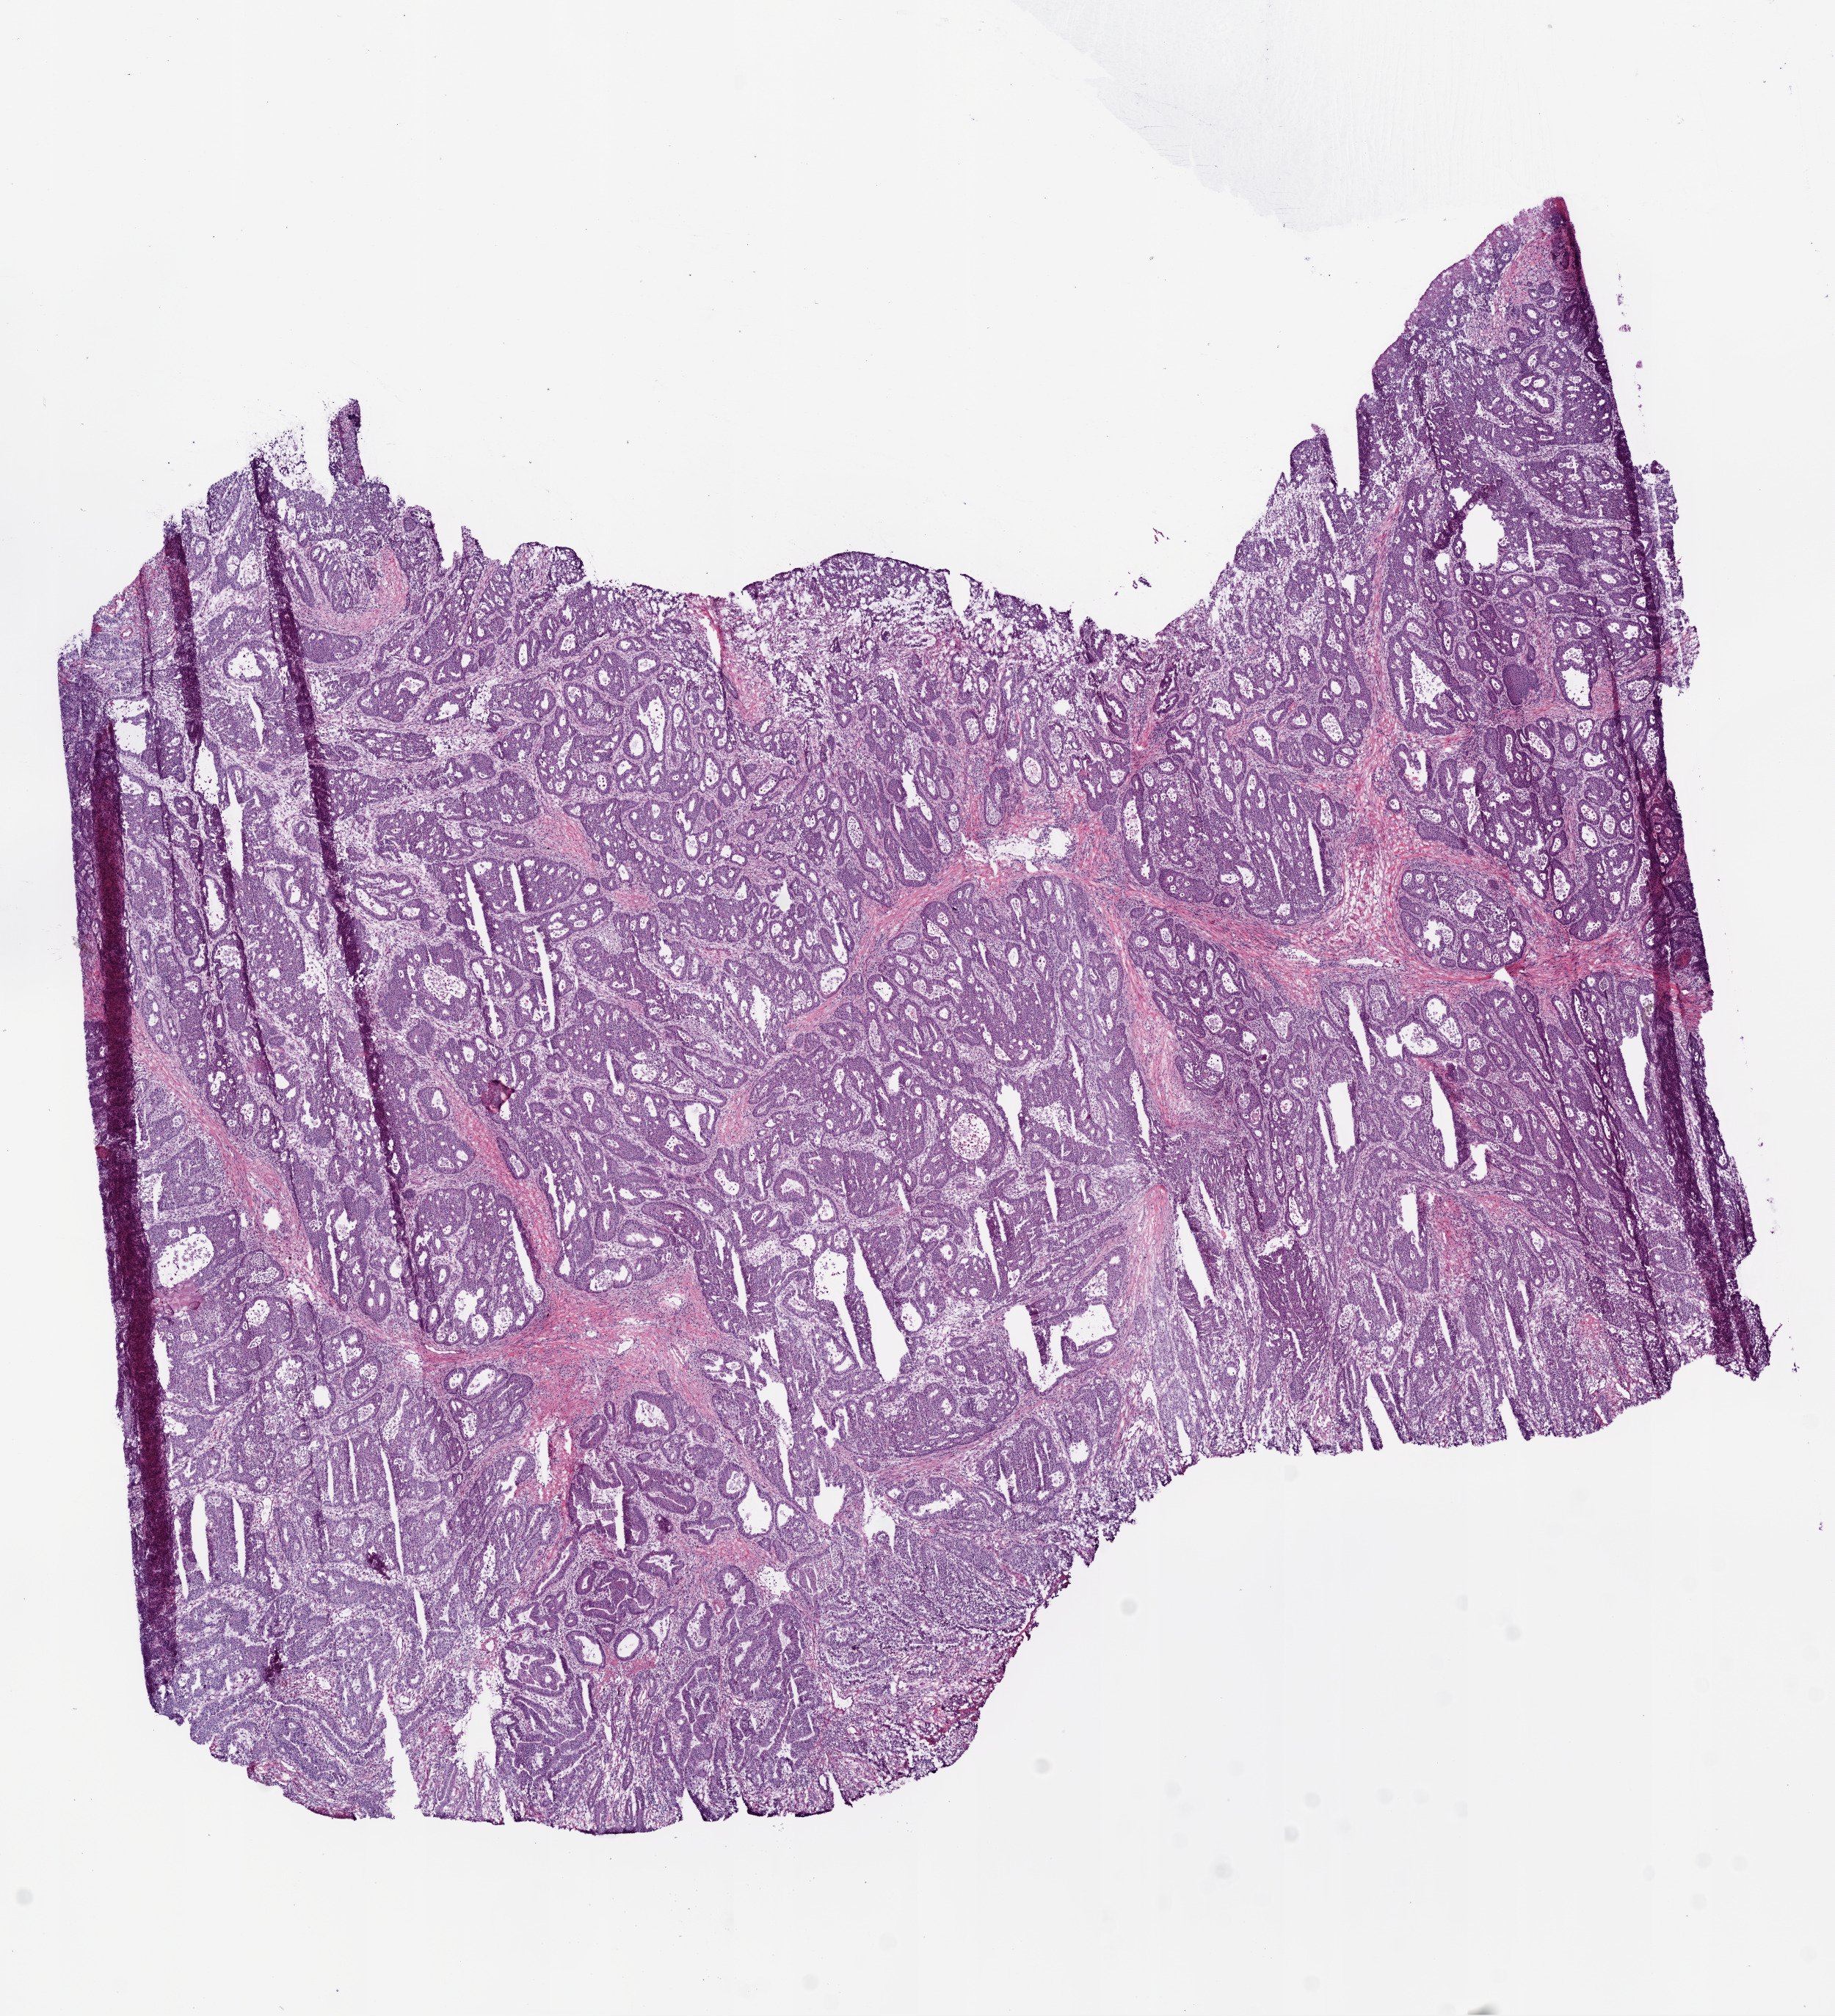
Digitized H&E tissue section (whole slide), a low-resolution overview of the entire scanned area, about 10.0 x 11.0 mm; frozen section; primary tumour sample from the colon. Female, age 83 years at initial diagnosis. Slide review estimates, as recorded: tumour cells 90%, tumour nuclei 75%, normal cells 0%, stromal cells 8%, necrosis 2%.
AJCC pathologic stage: II (5th edition). Lymph nodes positive (case pathology): 0 of 23 examined. Pathologic diagnosis: Adenocarcinoma, NOS.